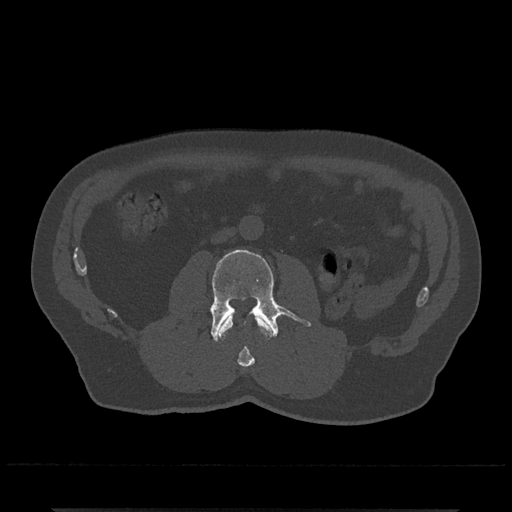
CT including the spine, one axial slice. 120 kVp. Bone window (W 1800 / L 400 HU). 0.5 mm slice thickness. 512 × 512 image matrix, field of view 393 × 393 mm. Male patient, age 67 years. From the clinical record (not read from this slice): primary cancer: prostate.
Annotated regions visible in this slice (semi-automatically segmented with operator editing):
- L2 vertebra: bounding box <218,315,271,368> (left, top, right, bottom; pixels)
- L3 vertebra: <210,249,311,342>